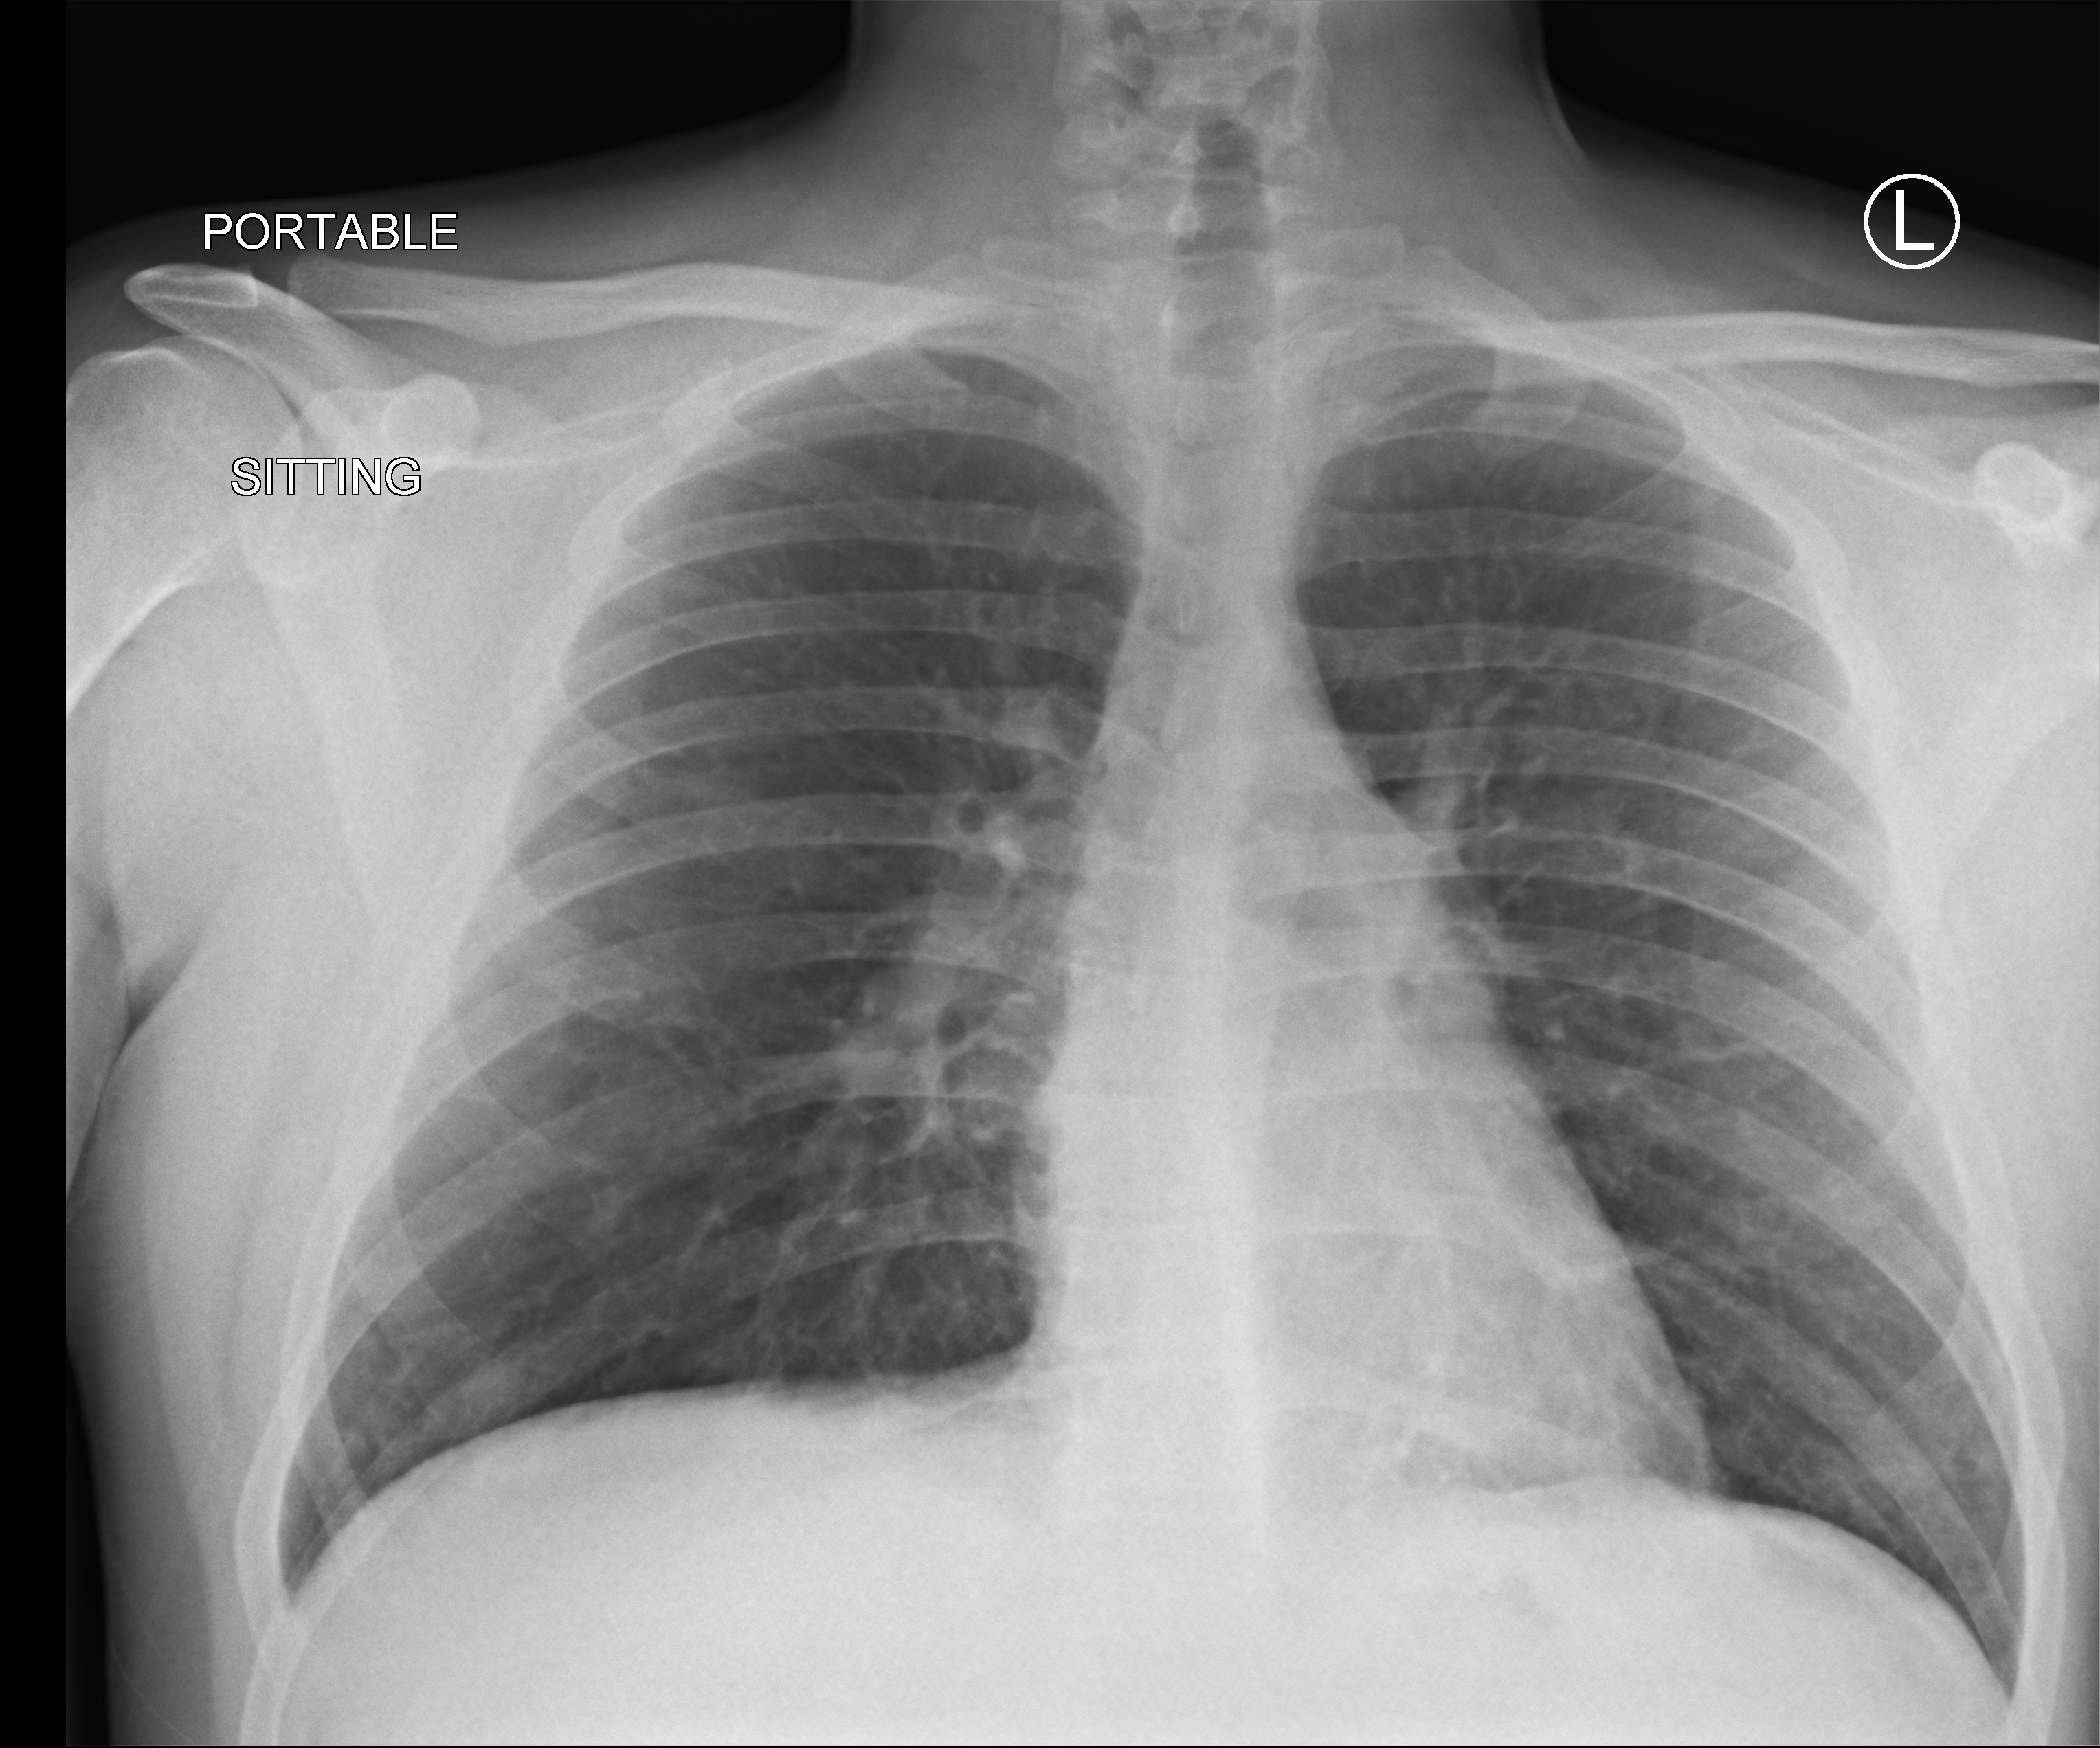
Portable chest radiograph, anteroposterior (AP) projection. Patient hospitalised with COVID-19; male, aged 18–59 years.
Admission-level facts for this patient (not findings on this image; timing relative to this image not recorded): admitted to intensive care during this hospital stay: no; mechanically ventilated during this hospital stay: no.